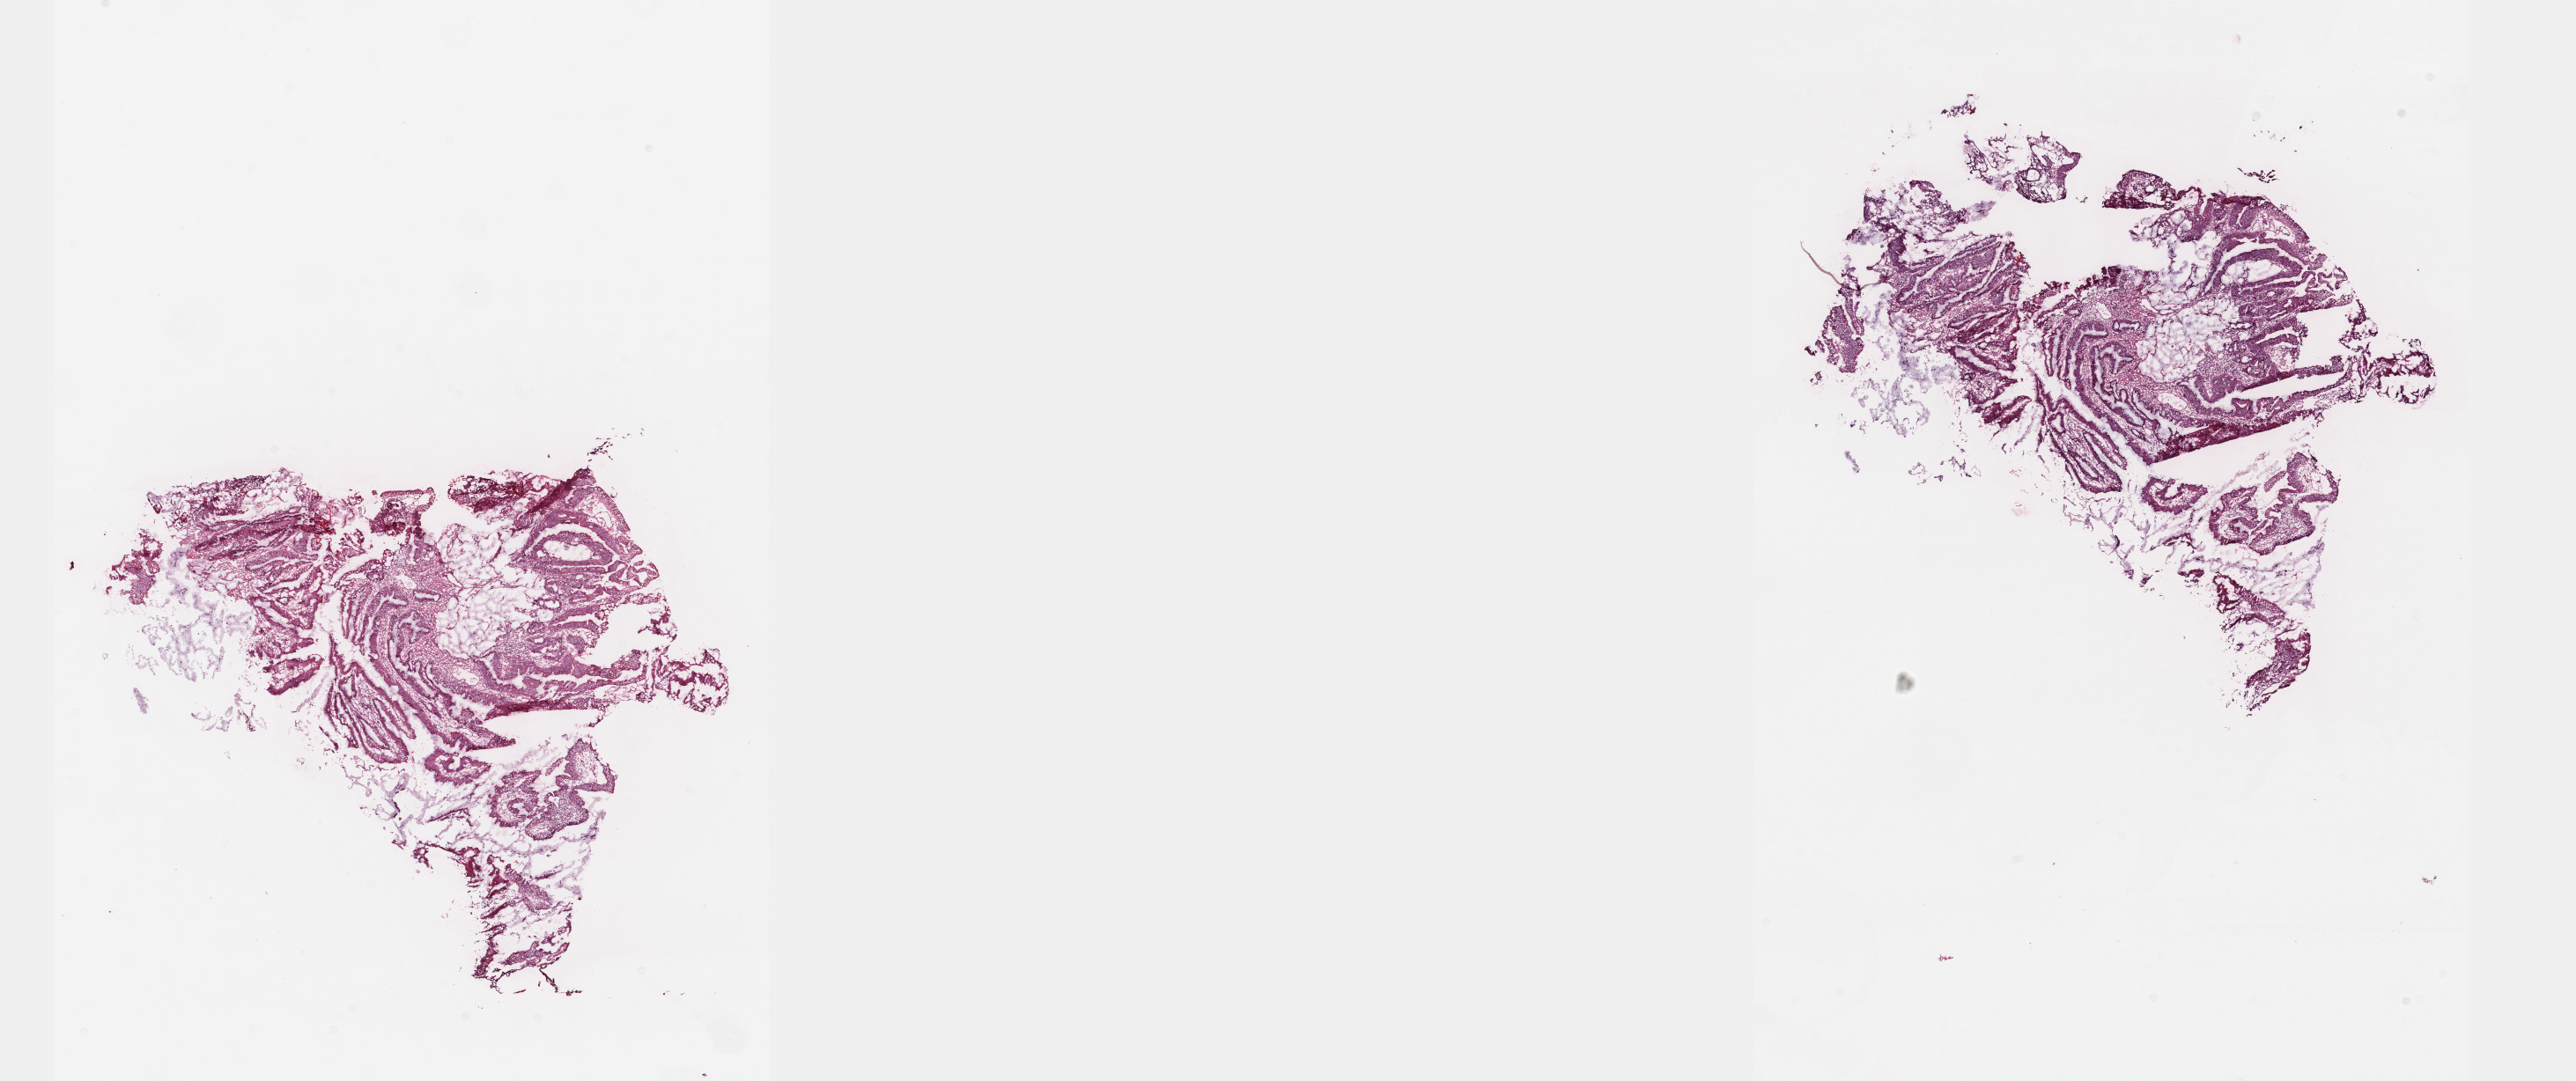
Digitized H&E tissue section (whole slide), whole scanned area (about 23.6 x 9.9 mm, slide scanned at 40x) shown as a low-resolution overview; frozen section from the bottom of the tissue portion; primary tumour sample from the colon. Male patient; age at initial diagnosis 81 years. Slide review estimates, as recorded: tumour cells 60%, tumour nuclei 70%, normal cells 0%, stromal cells 39%, necrosis 1%. Infiltration values recorded for this section: lymphocyte infiltration 5%, monocyte infiltration 0%, neutrophil infiltration 0%.
• AJCC pathologic stage: II (5th edition)
• lymph nodes positive (case pathology): 0 of 14 examined
• histologic diagnosis: Adenocarcinoma, NOS (descending colon)